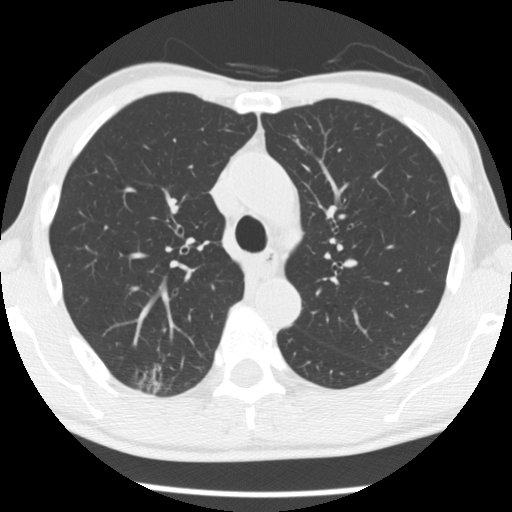
Low-dose screening chest CT, axial slice, baseline screening round, lung window (W 1500 / L -600 HU), 120 kVp, slice 86 of 277 in the series, 512 × 512 image matrix. Male, age 66 years at enrolment.
Lesion marked by an expert reader, bounding box [x1, y1, x2, y2] px = [131, 356, 191, 403]. The screening reader recorded 4 non-calcified nodules or masses ≥4 mm on this exam; which of them this box marks is not recorded. Later outcome: lung cancer diagnosed 503 days after this screen — adenocarcinoma, NOS, right upper lobe, undifferentiated (G4), stage IA (AJCC 6th edition), 20 mm at pathology.